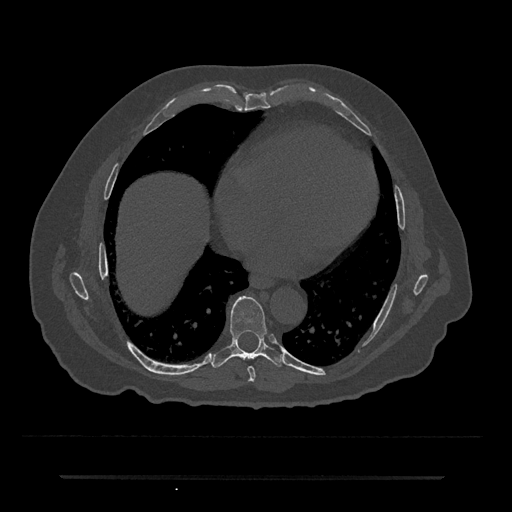
CT including the spine, one axial slice. Slice 342 of 797 in the series (ordered by position). Bone window (W 1800 / L 400 HU). 0.5 mm slice thickness. 512 × 512 image matrix. Patient: male, 69 years. Case-level facts recorded for this patient, not image findings: primary cancer: prostate.
Outlined on this slice (semi-automatic segmentation, software-assisted and operator-edited):
- T7 vertebra: bounding box <248,366,256,382> (left, top, right, bottom; pixels)
- T8 vertebra: <211,296,282,368>